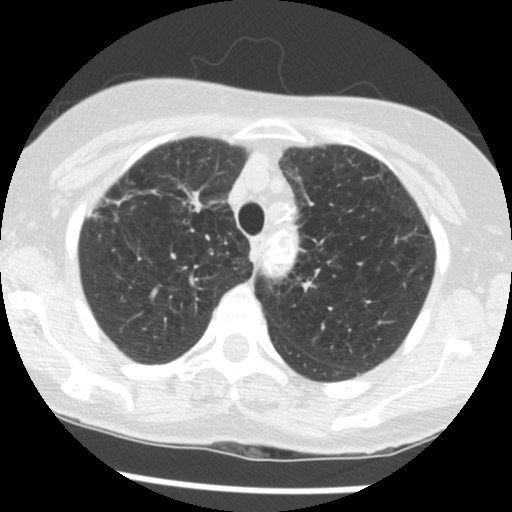
Chest CT (low-dose screening protocol), one axial image; second annual screen; lung window (W 1500 / L -600 HU); 2.5 mm slice thickness; standard (soft-tissue) reconstruction kernel (STANDARD). Female participant, aged 70 years at enrolment. Former smoker at enrolment.
• Expert reader's lesion annotation, bounding box (x1, y1, x2, y2) in pixels: (156, 168, 226, 224).
• Reader record for this screening exam (exam-level; its link to the box is not recorded): non-calcified nodule or mass ≥4 mm, right upper lobe, 11 × 7 mm, spiculated (stellate) margins, soft tissue attenuation, pre-existing on the prior screen: yes; interval growth: yes.
• Official screen result: positive, other.
• Participant outcome: lung cancer diagnosed 248 days after this screen — non-small cell carcinoma, right upper lobe, stage IV (AJCC 6th edition), 30 mm at pathology.